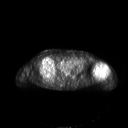
FDG PET of an extremity soft-tissue mass (from a PET/CT study), one axial slice; position 148 of 267 along the scan axis; 3.27 mm slice thickness; 128 × 128 image matrix, field of view 700 × 700 mm. Patient: female, 83 years. Case-level facts recorded for this patient, not image findings: histological type: pleiomorphic leiomyosarcoma; grade: high; site of the primary tumour: left biceps.
Annotated regions visible in this slice (expert contour drawn on MRI and transferred to this co-registered scan by the dataset authors):
- gross tumour volume including surrounding oedema: bounding box <92,63,107,77> (left, top, right, bottom; pixels)
- gross tumour volume (mass): <92,63,107,76>